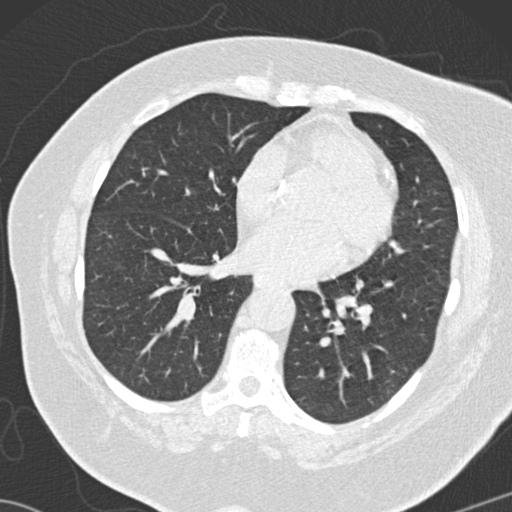
Low-dose screening chest CT, one axial slice; slice 59 of 146 in the series (ordered by position); 120 kVp; lung window (W 1500 / L -600 HU); 512 × 512 image matrix, field of view 350 × 350 mm.
Annotated regions visible in this slice (expert manual segmentation):
- lesion 2 (tumor, lower lobe of right lung): bounding box [x1, y1, x2, y2] px = [112, 260, 127, 275]